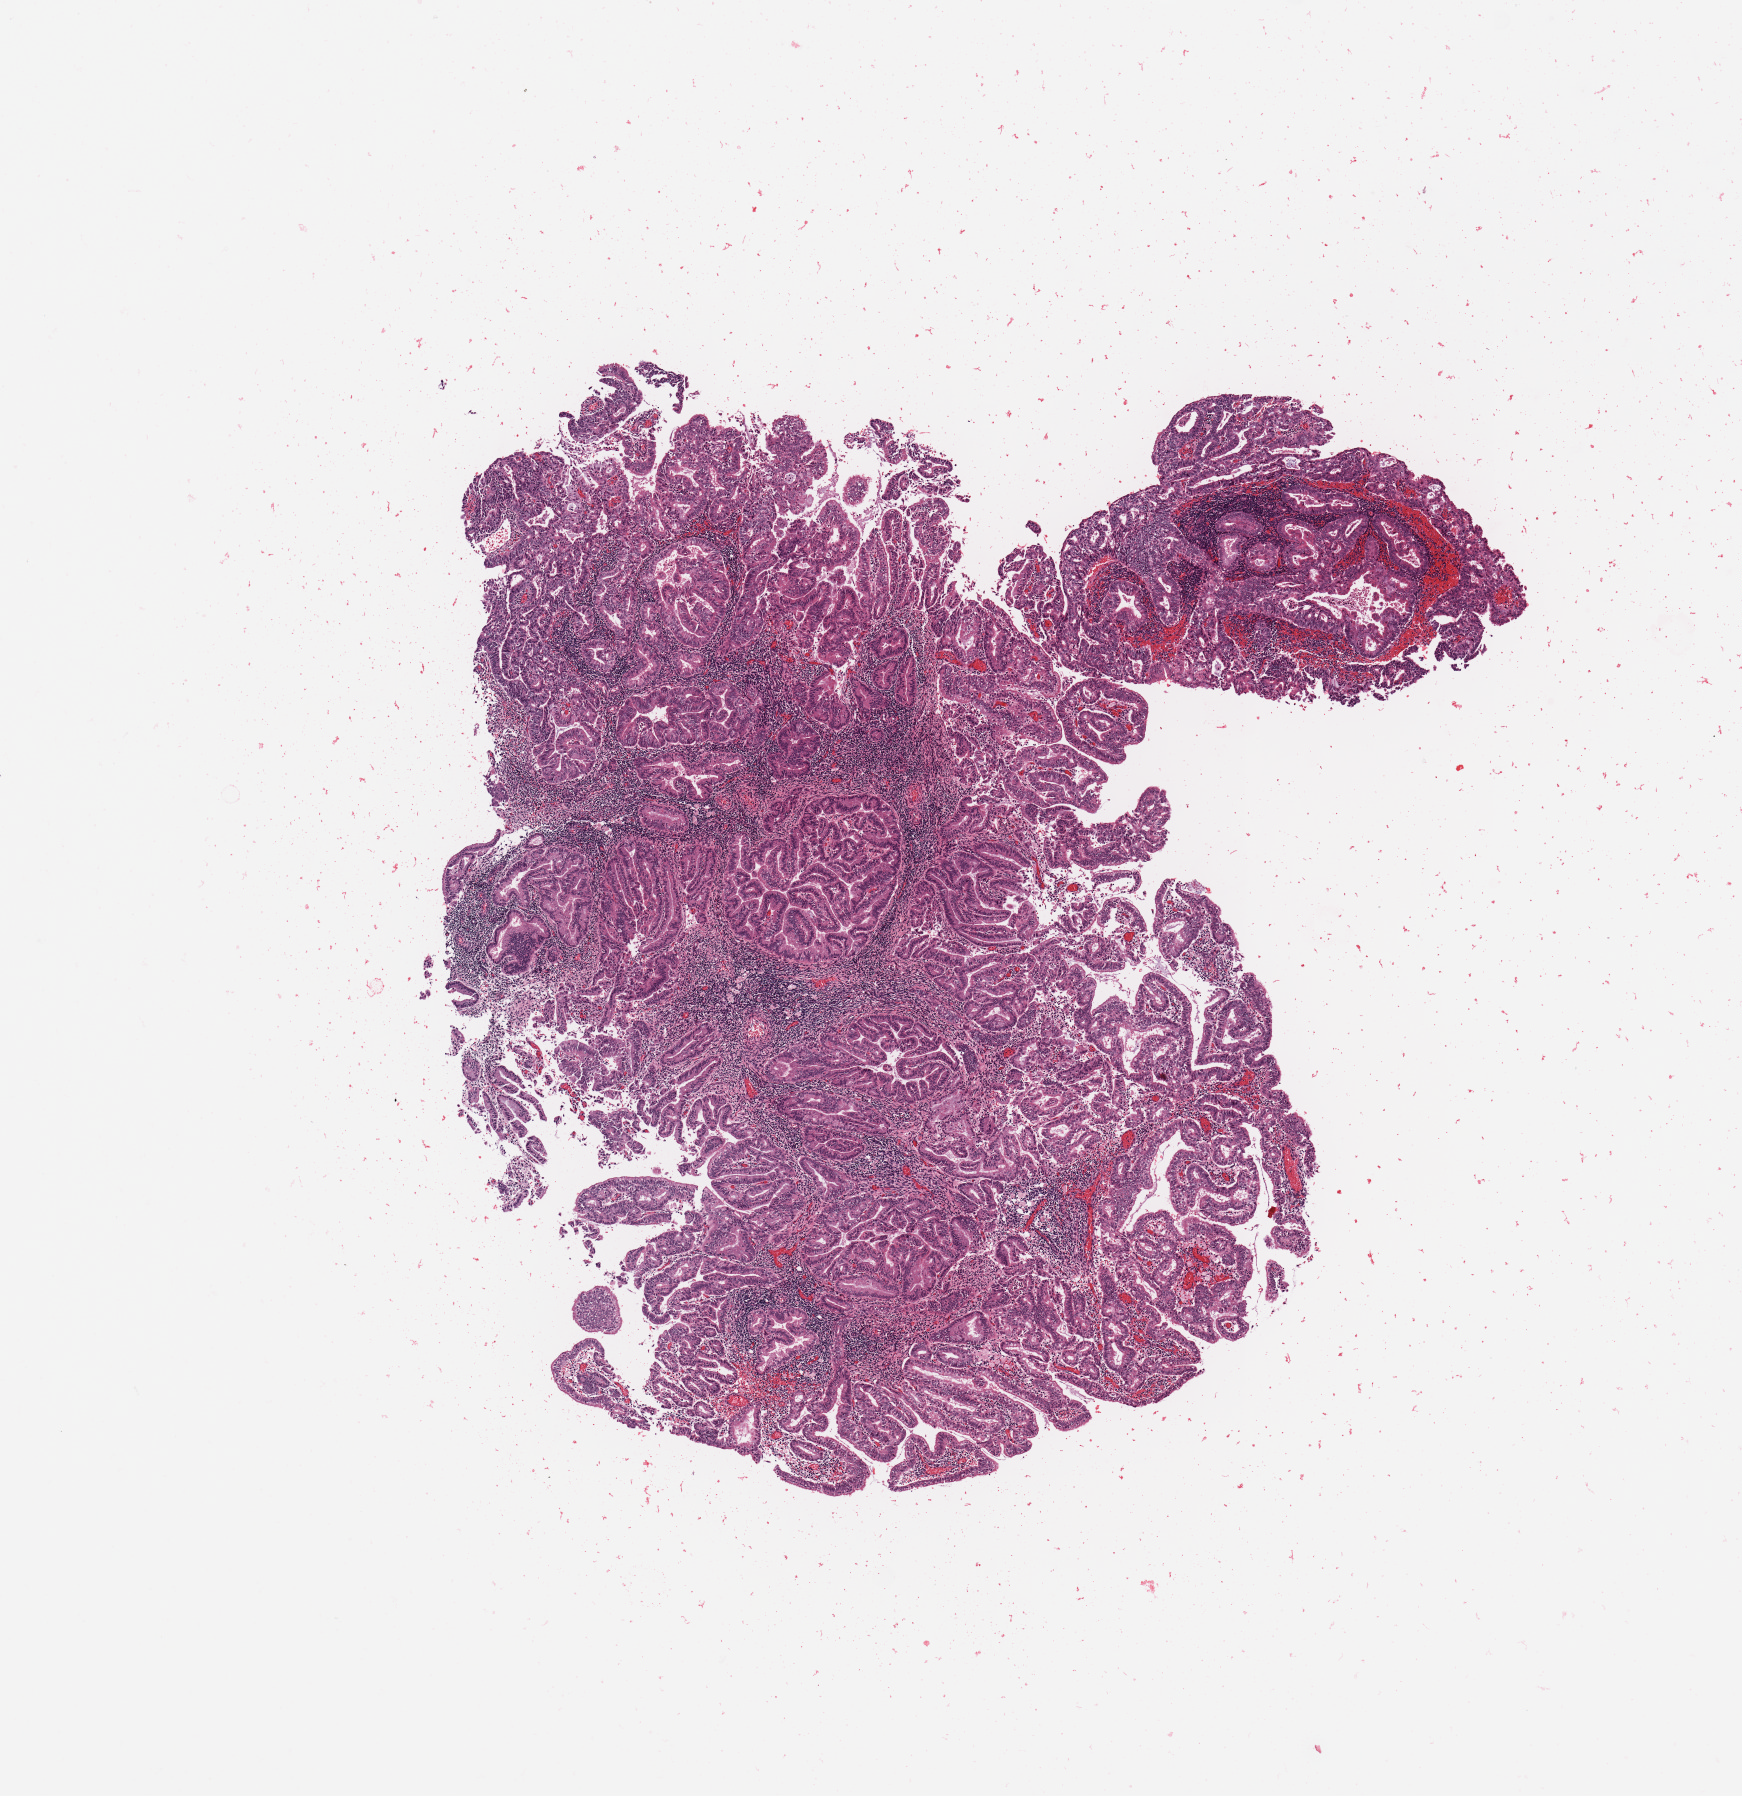
H&E-stained whole-slide image — a low-resolution overview of the entire scanned area, about 6.9 x 7.1 mm (from a 20x scan). Tumour tissue sample, sampled site: uterus. Female, 42 y/o.
Diagnosis: Endometrioid adenocarcinoma, NOS.